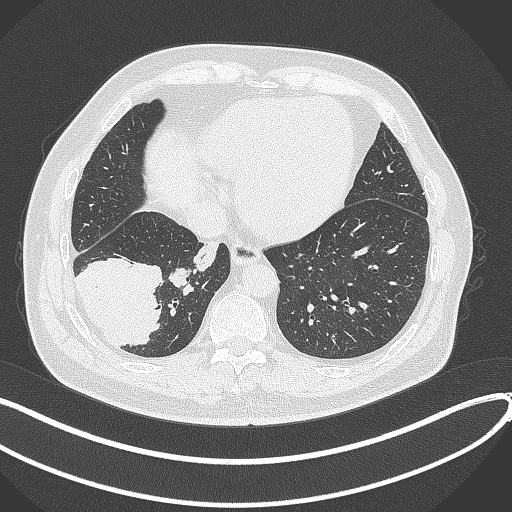
Chest CT, one axial slice. Slice 98 of 360 in the series (ordered by position). Reconstruction kernel B70f. 120 kVp. Lung window (W 1500 / L -600 HU). 512 × 512 image matrix, field of view 400 × 400 mm. Patient: male, 59 years.
Annotated regions visible in this slice (bounding box drawn by a radiologist):
- lung tumour (recorded histology: adenocarcinoma): bounding box (x1, y1, x2, y2) in pixels: (70, 254, 163, 348)